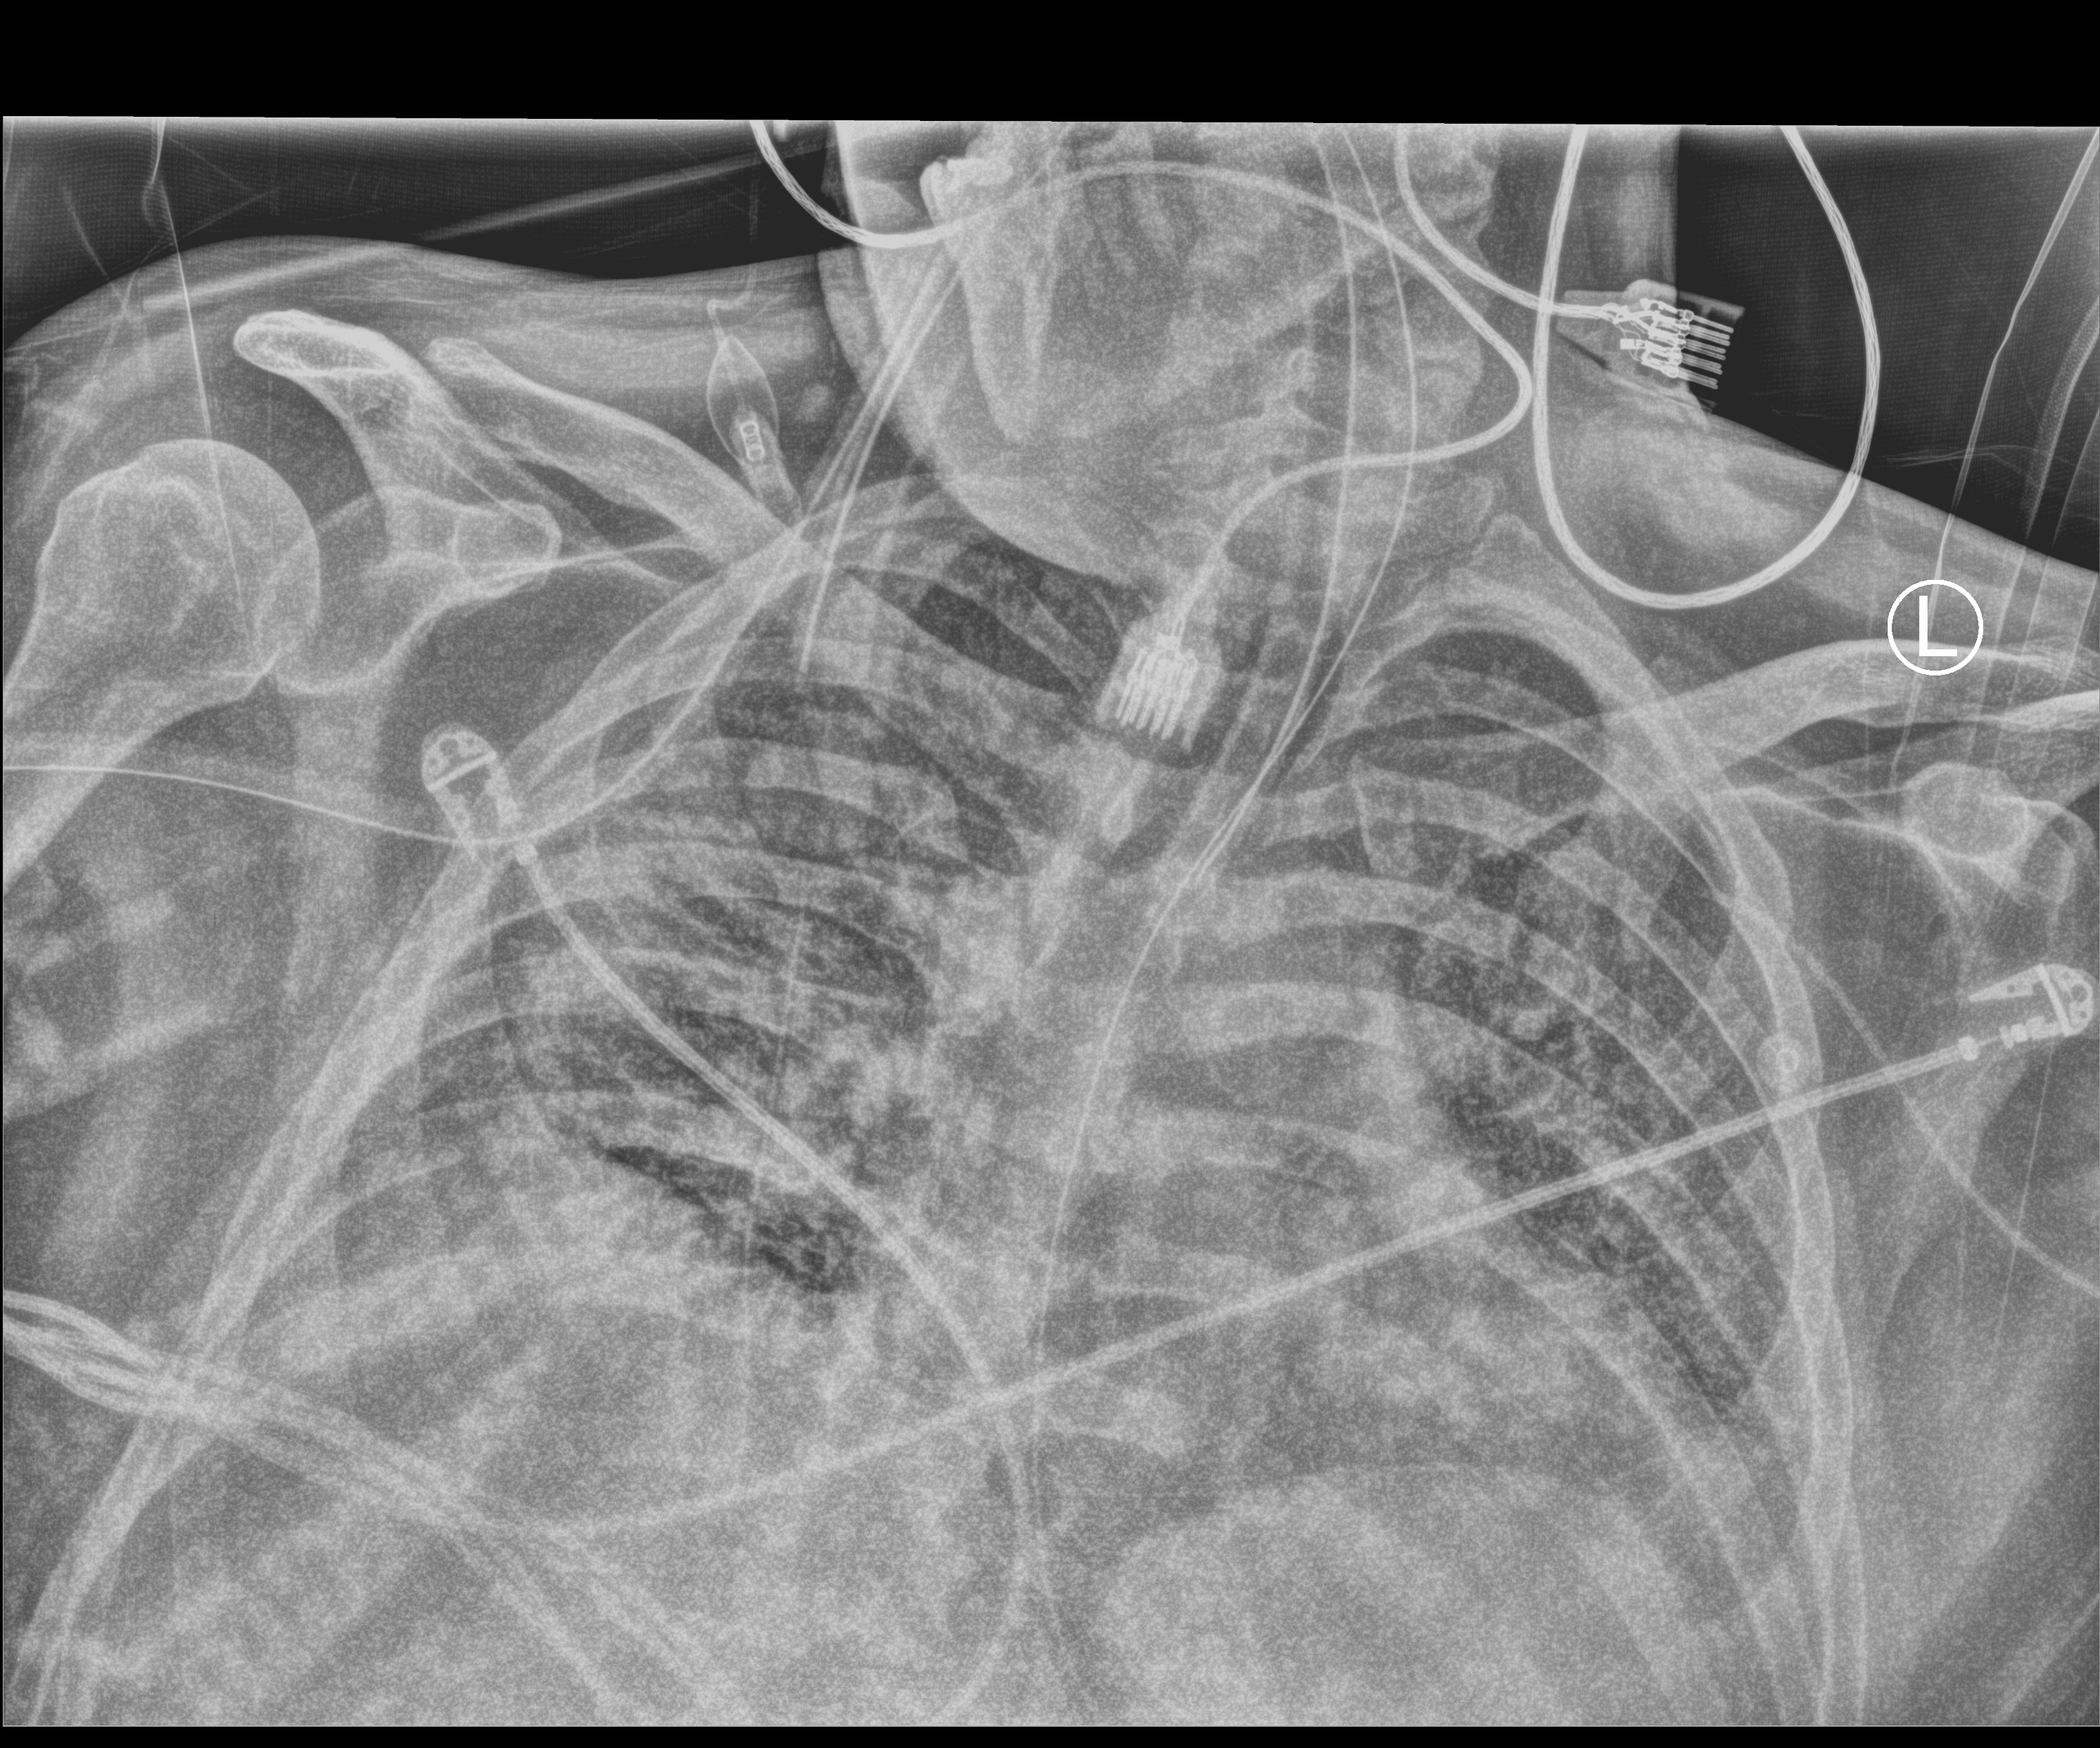
Chest X-ray (portable); anteroposterior (AP) projection. Male patient hospitalised with COVID-19, age 18–59 years.
Hospital-stay facts (about this admission, not read from this image; timing relative to this image not recorded): admitted to intensive care during this hospital stay: yes; COPD (admission record): no; mechanically ventilated during this hospital stay: yes.